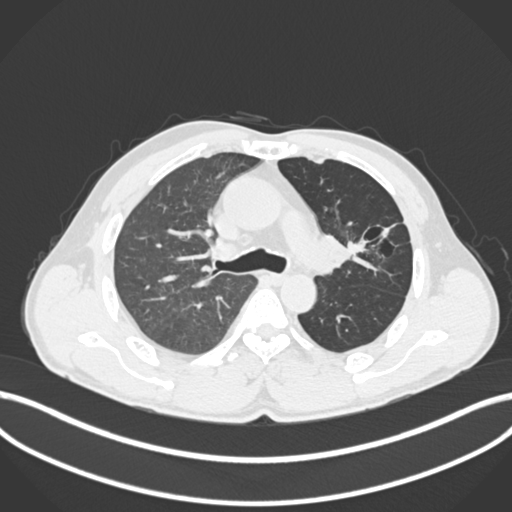
Chest CT, one axial slice; position 126 of 255 along the scan axis; 120 kVp; lung window (W 1500 / L -600 HU); 1 mm slice thickness; 512 × 512 image matrix, field of view 400 × 400 mm. Male patient, age 57 years. Case-level facts recorded for this patient, not image findings: clinical TNM (as recorded): T2b N0 M0.
Annotated regions visible in this slice (bounding box drawn by a radiologist):
- lung tumour (recorded histology: squamous cell carcinoma): bounding box [x1, y1, x2, y2] px = [316, 225, 371, 274]